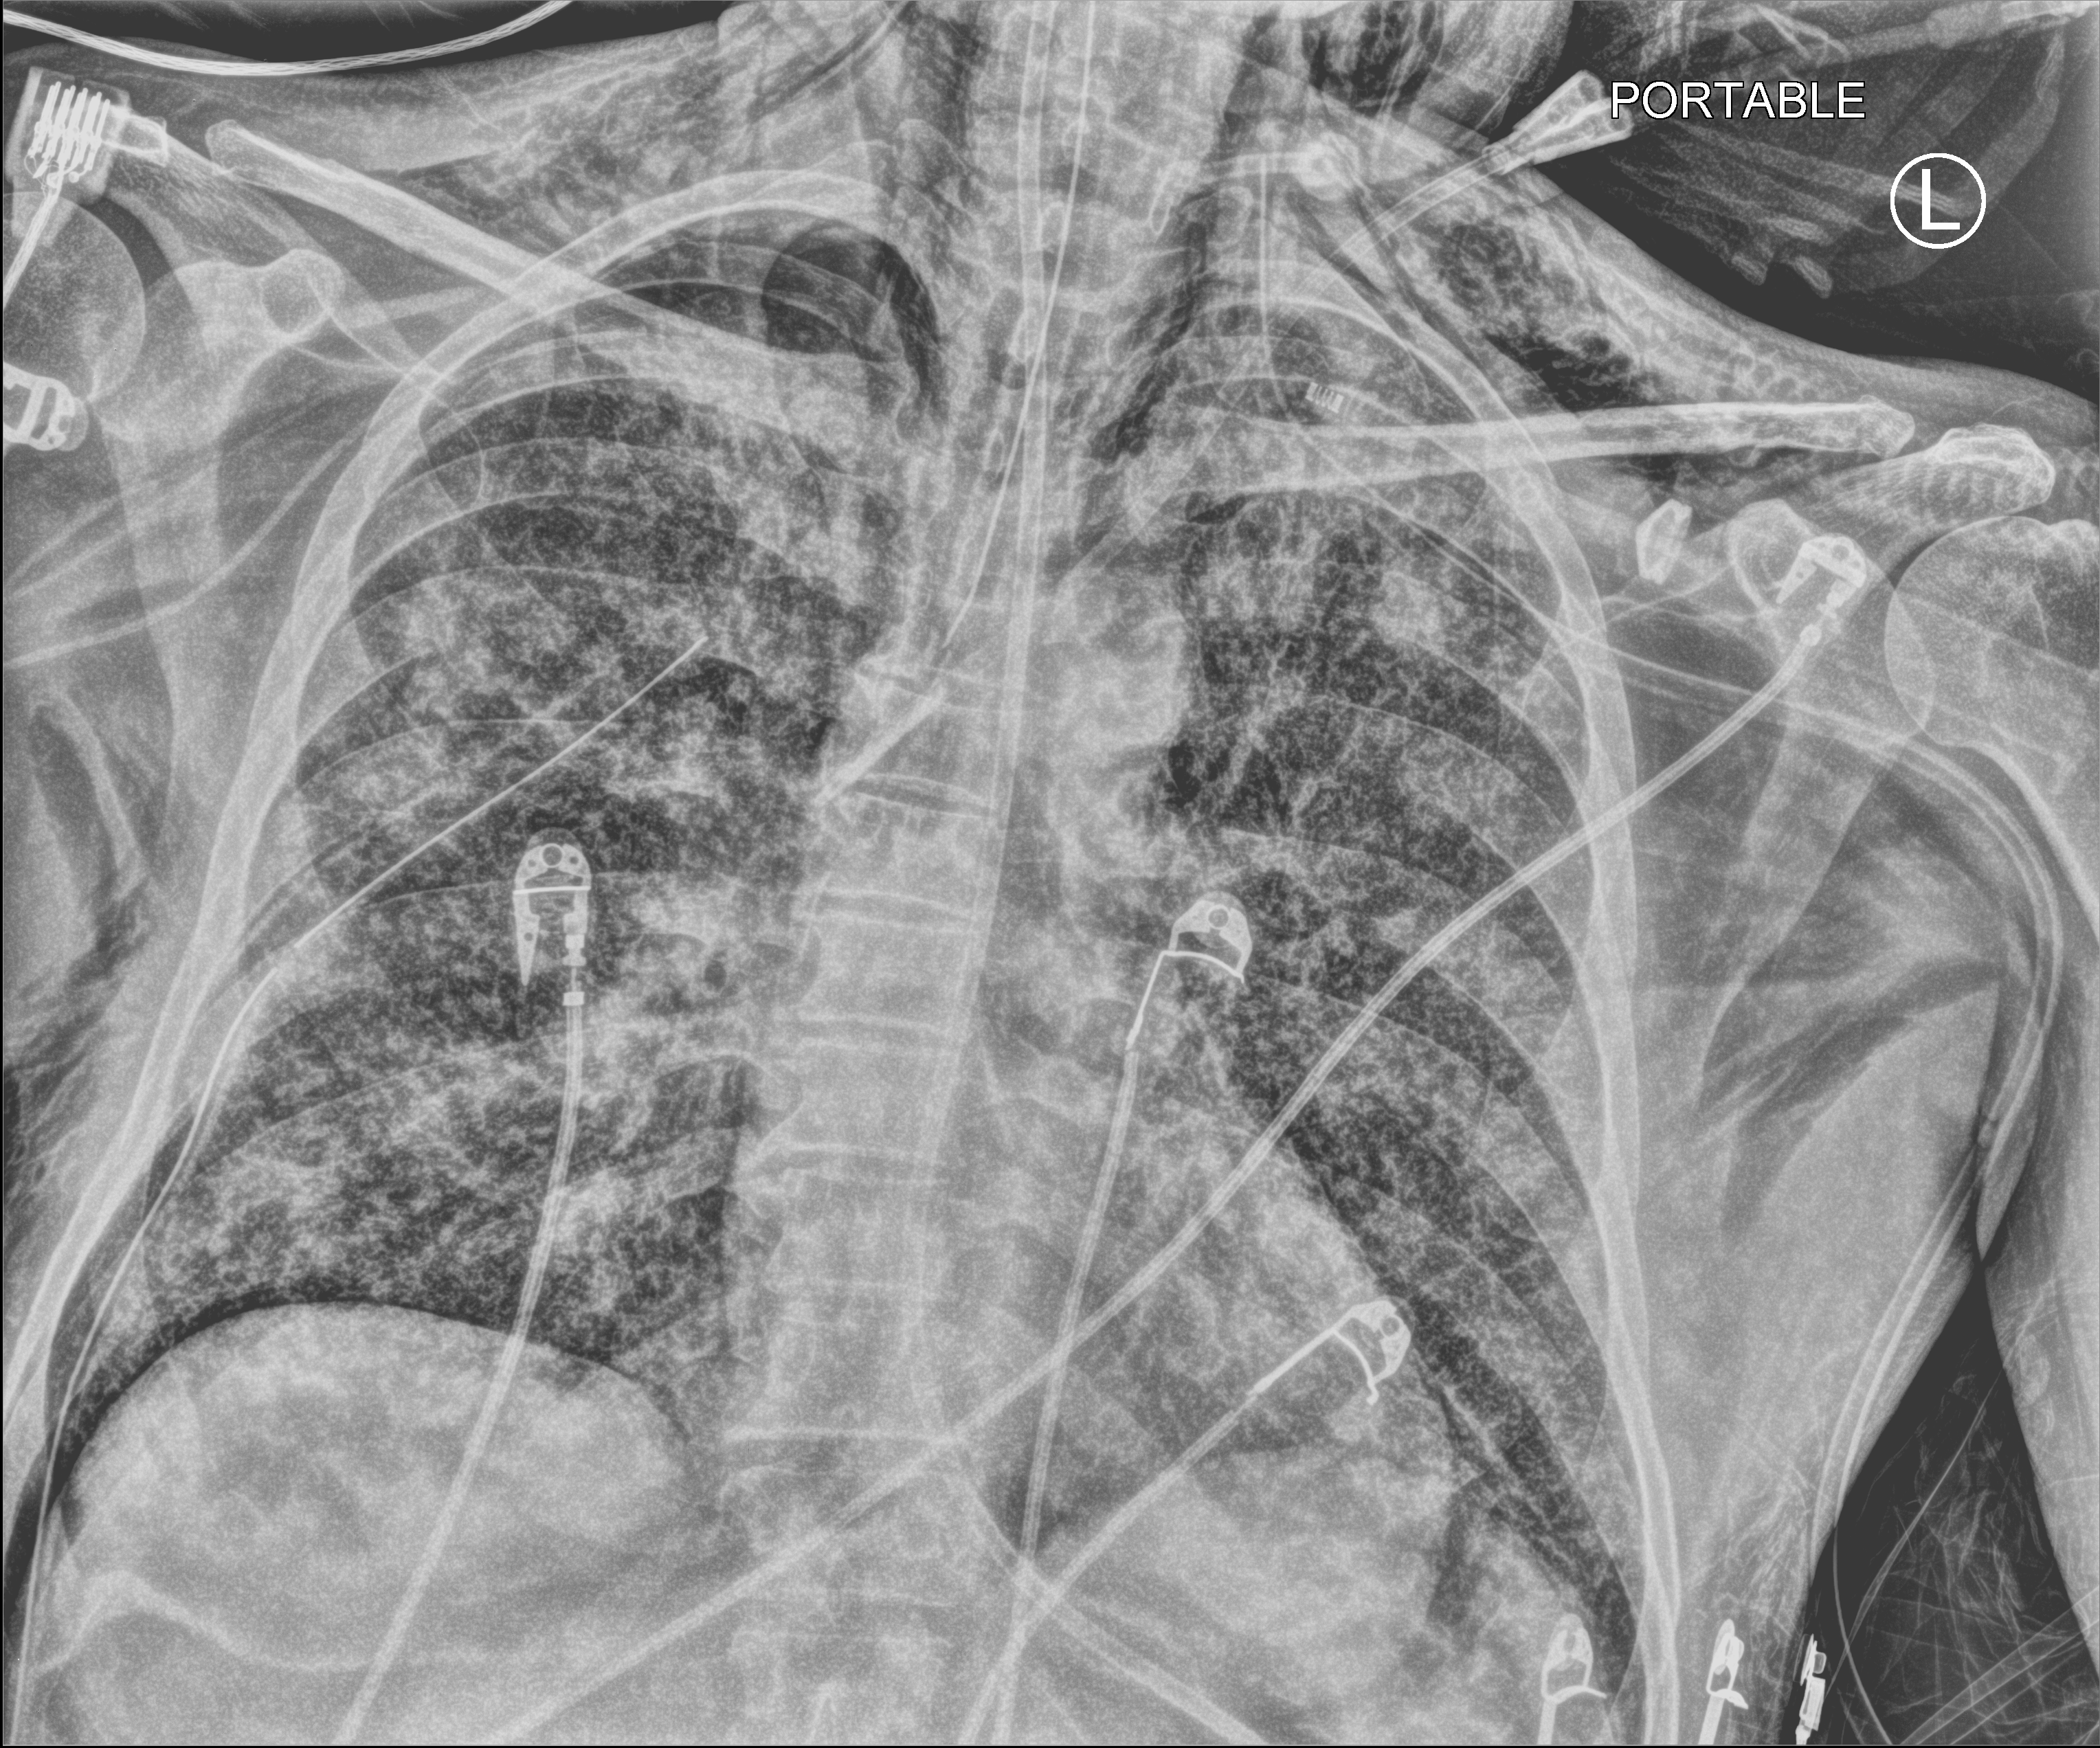
Bedside chest radiograph (computed radiography); anteroposterior (AP) projection. Male patient hospitalised with COVID-19, age 18–59 years.
From the hospital-stay record, not from the radiograph (when in the stay this image was taken is not recorded):
- COPD (admission record): no